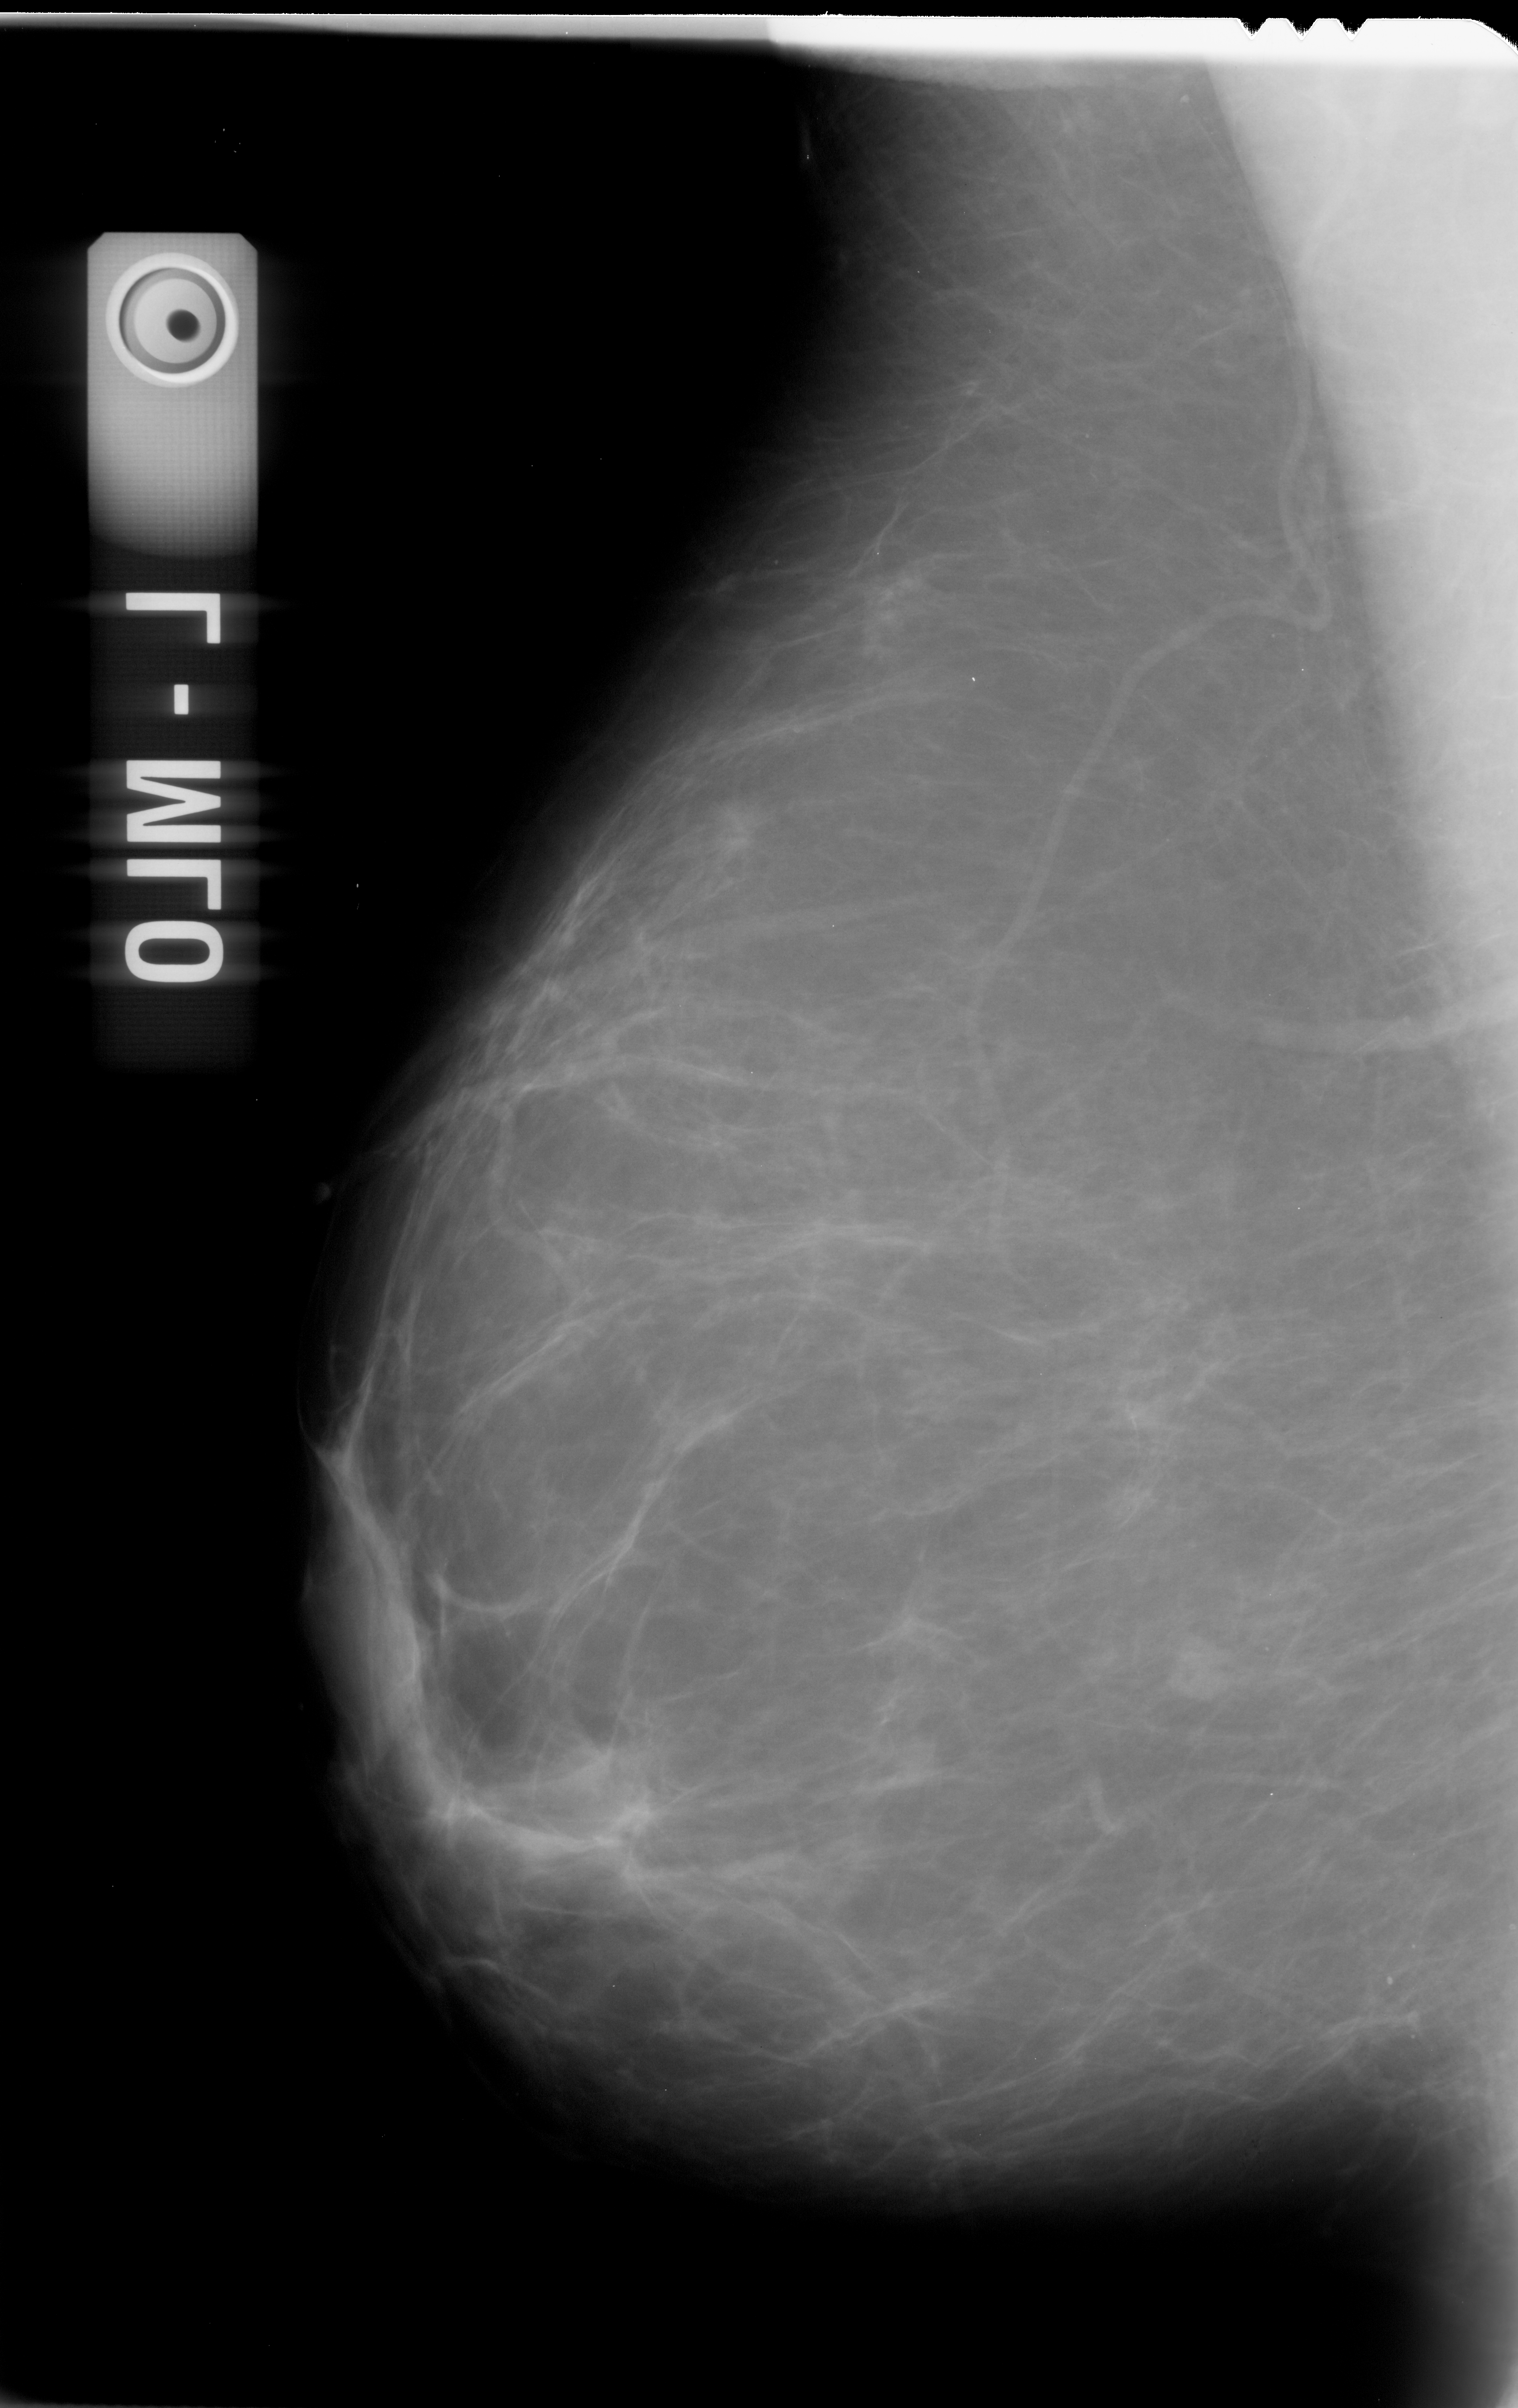
Mammogram (digitized film), left breast, MLO view.
- Mass, shape irregular, margins spiculated; BI-RADS assessment category 4; pathology (as recorded): malignant.